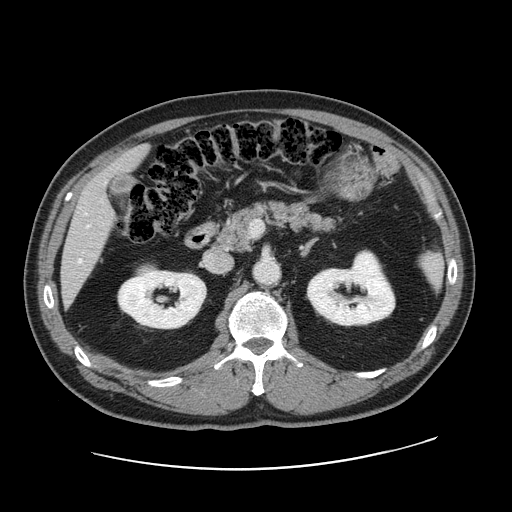
Contrast-enhanced abdominal CT, one axial slice. Slice 81 of 178 in the series (ordered by position). 120 kVp. Intravenous contrast given. Soft-tissue window (W 400 / L 40 HU). 2.5 mm slice thickness. 512 × 512 image matrix, field of view 403 × 403 mm. Male patient, age 63 years. Case-level facts recorded for this patient, not image findings: diagnosis: colorectal cancer liver metastases, imaged before liver resection; multiple liver metastases: yes; largest metastasis: 8 cm; disease in both lobes: yes.
Structures marked on this image (outlined manually by an expert reader):
- hepatic veins: bounding box [x1, y1, x2, y2] px = [79, 259, 82, 262]
- liver: [62, 148, 146, 300]
- planned liver remnant (the part of the liver to remain after resection): [111, 149, 146, 172]